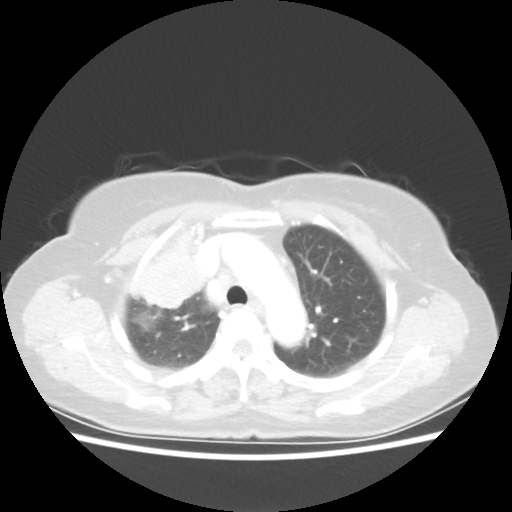
Chest CT, one axial slice; slice 40 of 55 in the series (ordered by position); lung window (W 1500 / L -600 HU); 512 × 512 image matrix, field of view 337 × 337 mm. Patient: female, 62 years. From the clinical record (not read from this slice): clinical TNM (as recorded): T4 N3 M0.
Structures marked on this image (rectangle marked by the reading radiologist):
- lung tumour (recorded histology: squamous cell carcinoma): bounding box <127,227,210,312> (left, top, right, bottom; pixels)